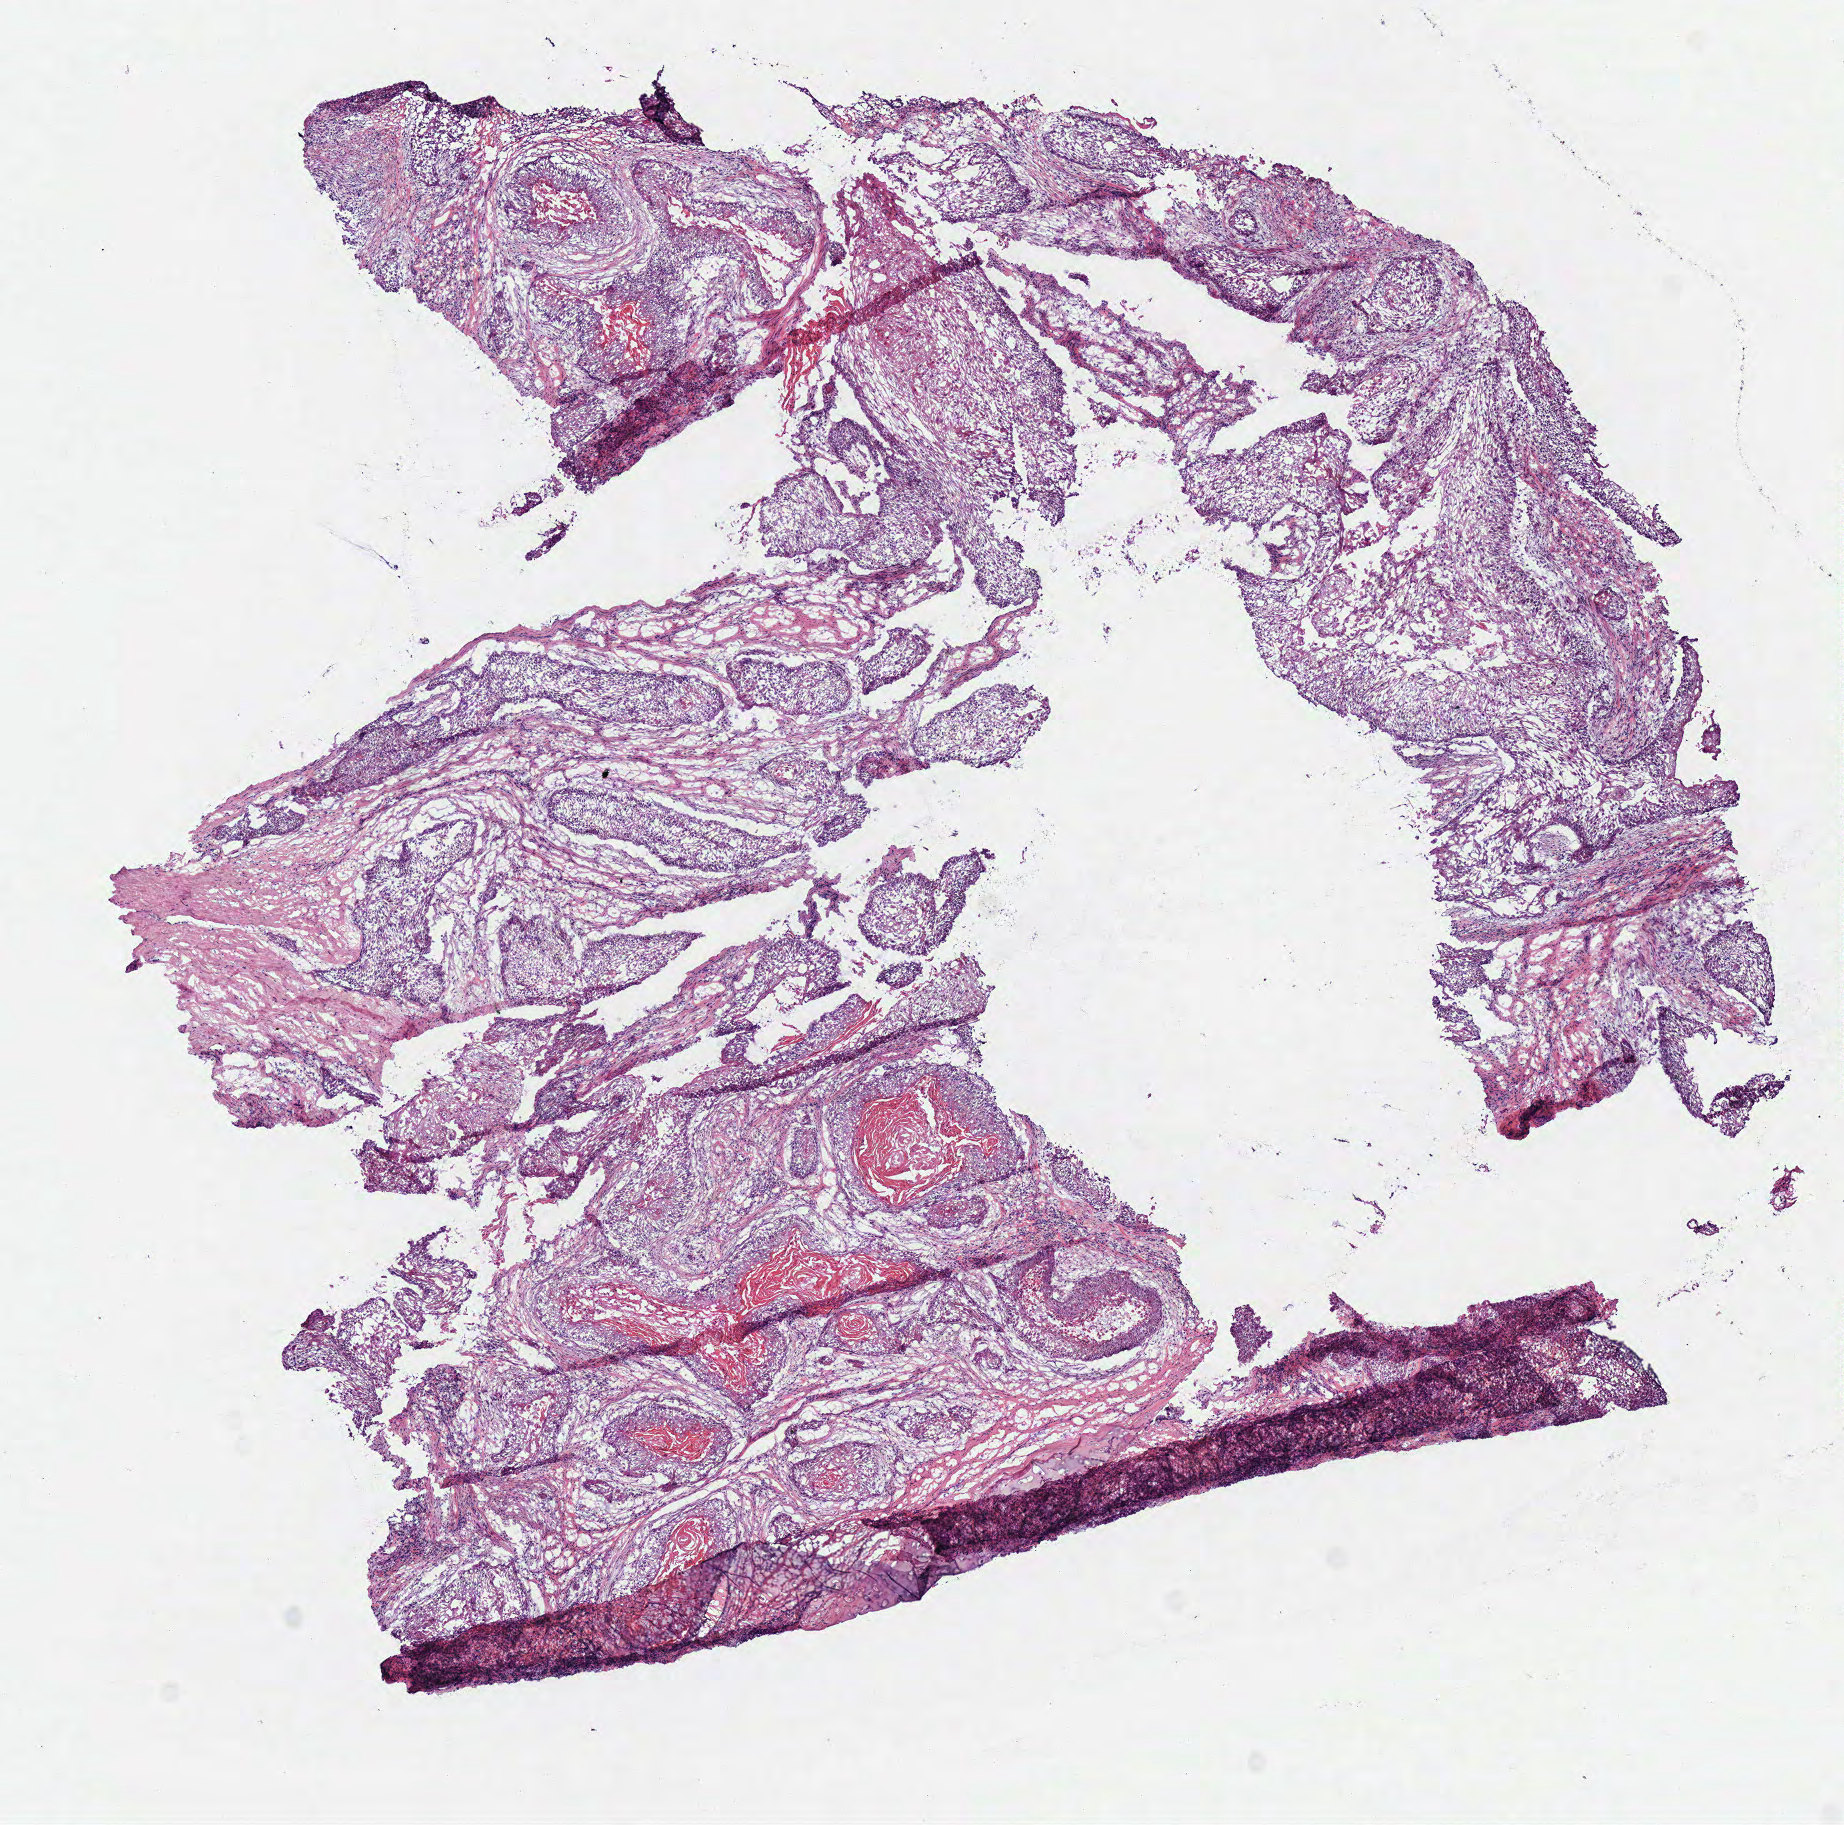
H&E whole-slide image — shown as a low-resolution overview of the whole scanned area (about 7.3 x 7.2 mm); frozen section from the top of the tissue portion; primary tumour sample from the head and neck. Female patient; age at initial diagnosis 82 years. Histologic grade: G2 (moderately differentiated). Composition of this section per pathologist review: tumour cells 75%, tumour nuclei 80%, normal cells 0%, stromal cells 25%, necrosis 0%.
- AJCC pathologic stage: II (7th edition)
- pathologic diagnosis: Squamous cell carcinoma, NOS (larynx, NOS)